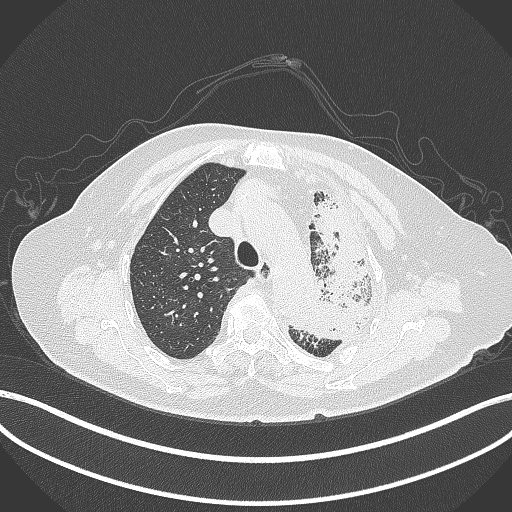
Chest CT, one axial slice. Slice 296 of 399 in the series (ordered by position). Reconstruction kernel B70f. 120 kVp. Lung window (W 1500 / L -600 HU). 512 × 512 image matrix, field of view 400 × 400 mm. Patient: female, 75 years. Case-level facts recorded for this patient, not image findings: clinical TNM (as recorded): T3 N3 M1.
Outlined on this slice (rectangle marked by the reading radiologist):
- lung tumour (recorded histology: adenocarcinoma): bounding box (x1, y1, x2, y2) in pixels: (287, 179, 378, 343)